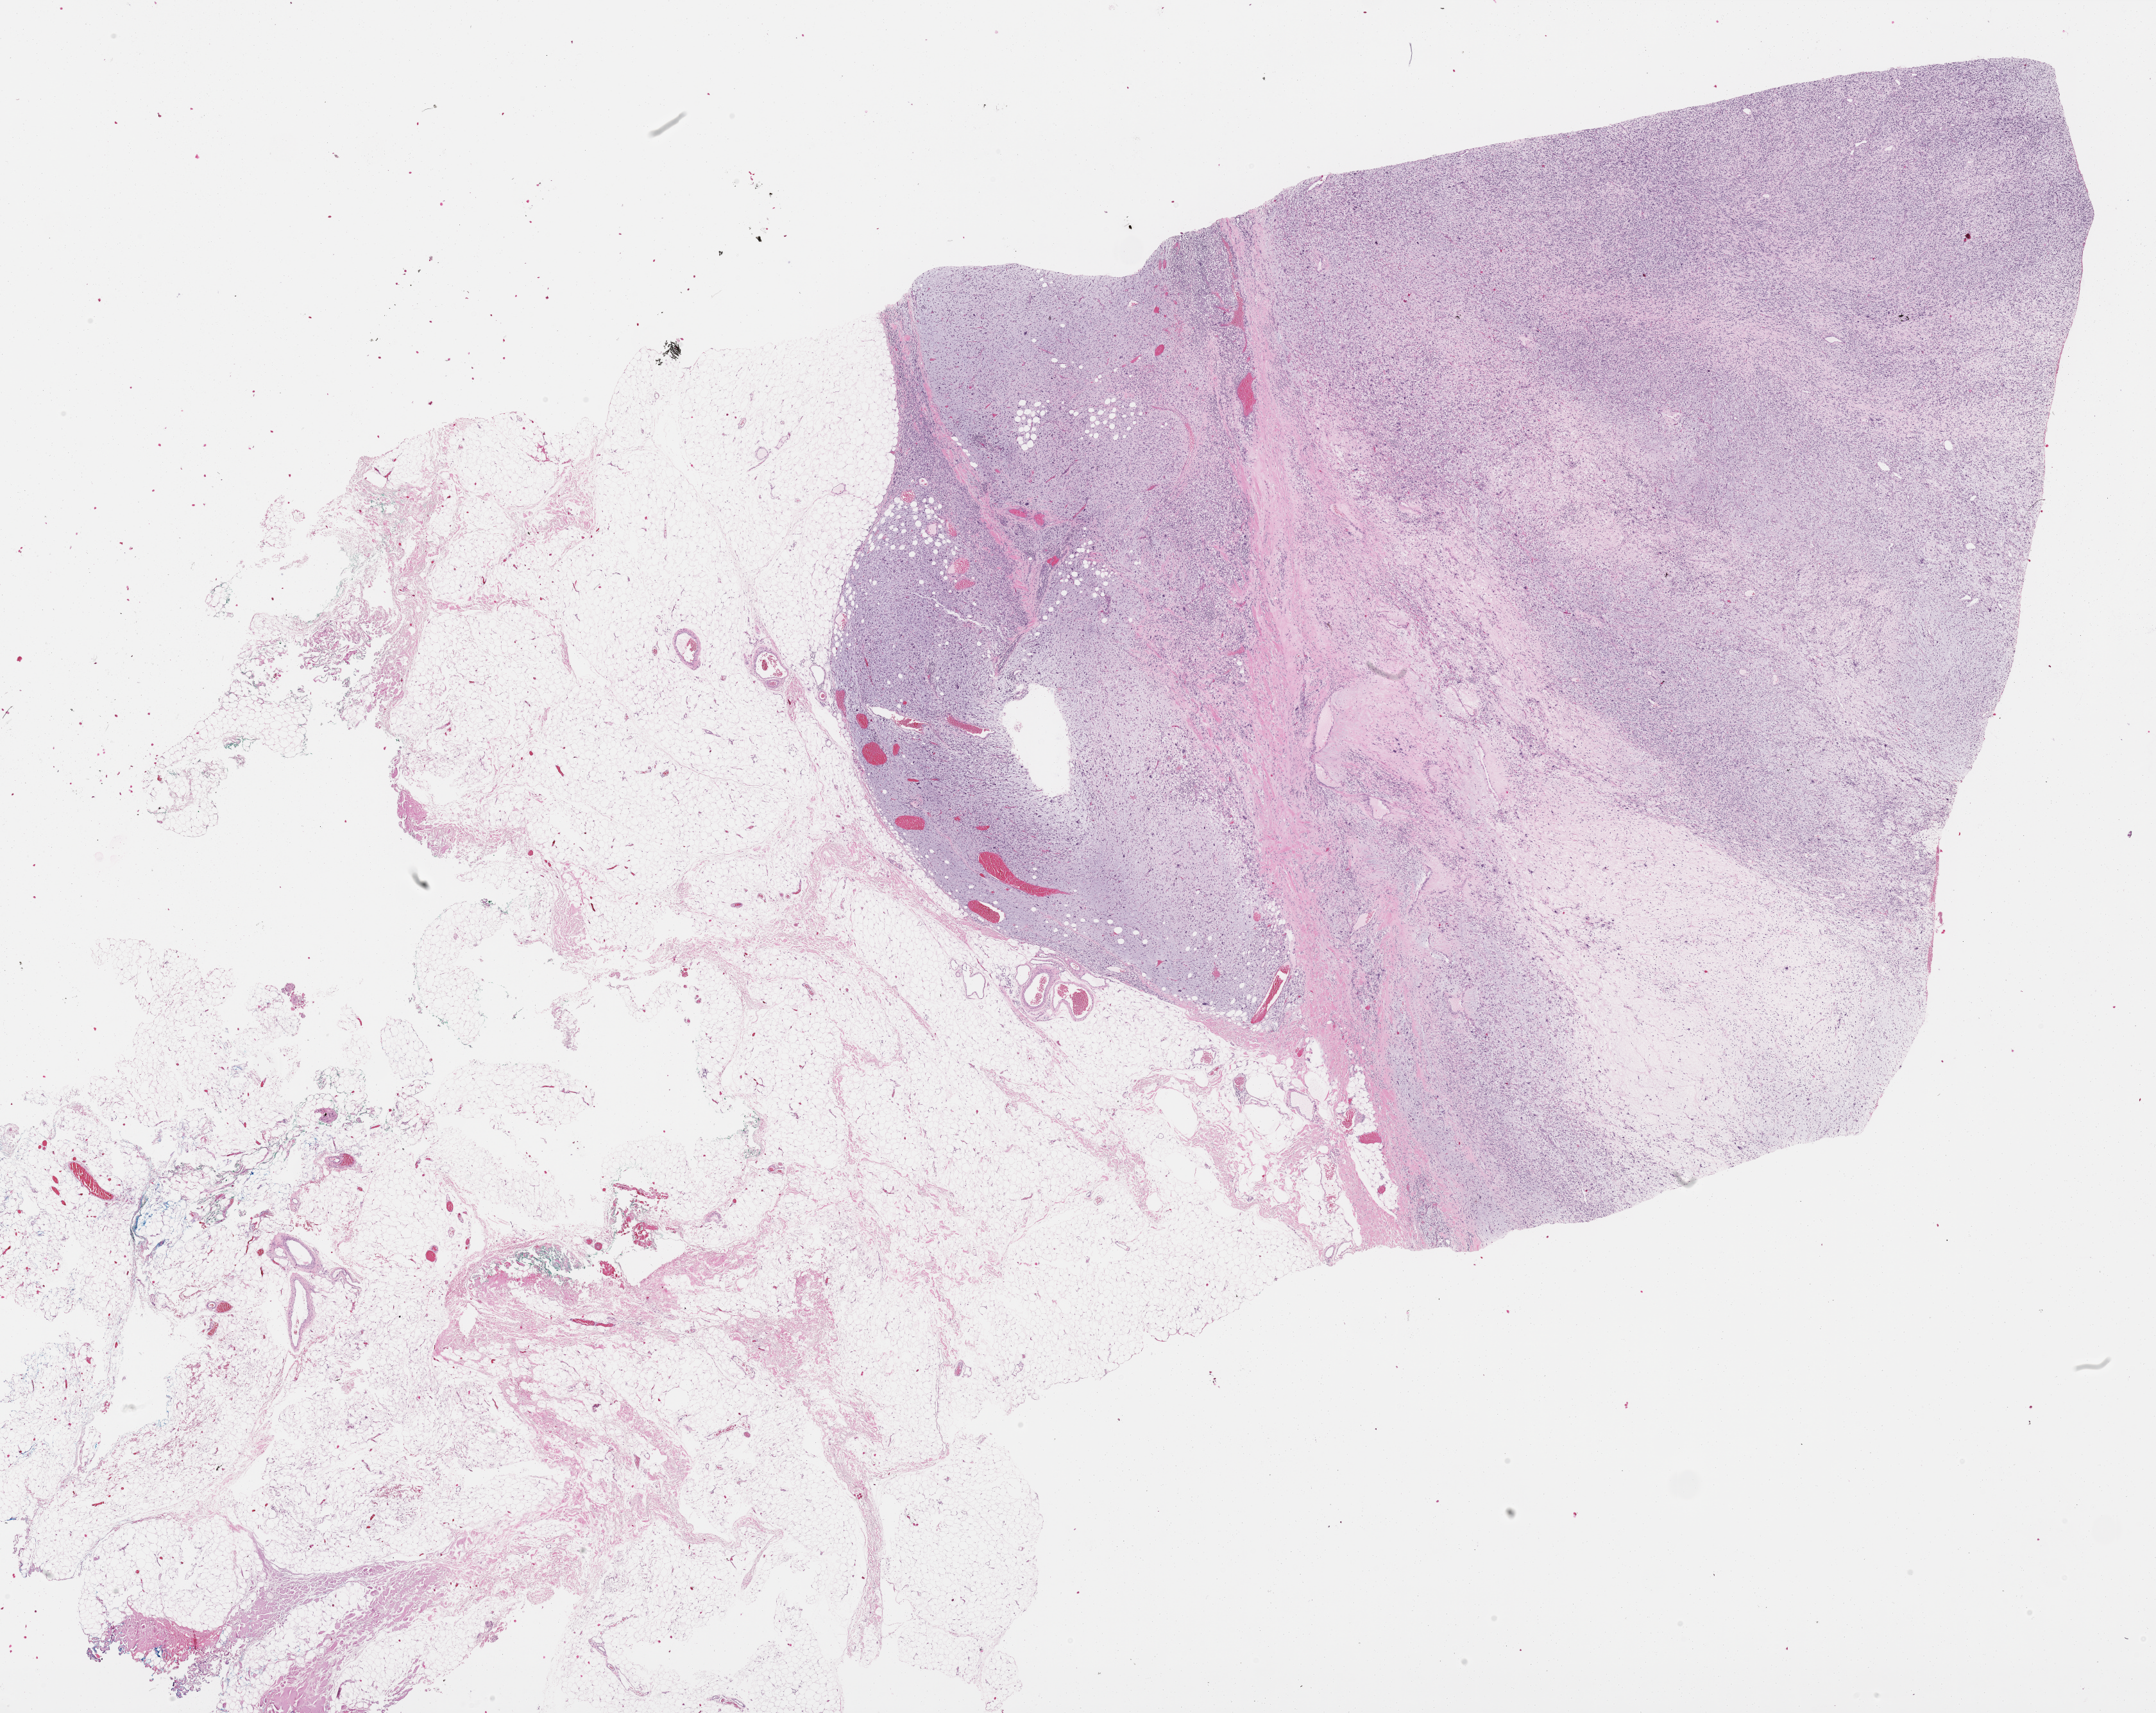
H&E-stained whole-slide image — low-resolution overview of the scanned area, about 27.2 x 21.6 mm; formalin-fixed paraffin-embedded (FFPE) diagnostic section; sample: primary tumour, connective, subcutaneous and other soft tissues. Female, age 50 years at initial diagnosis.
- diagnosis: Fibromyxosarcoma (connective, subcutaneous and other soft tissues of thorax)